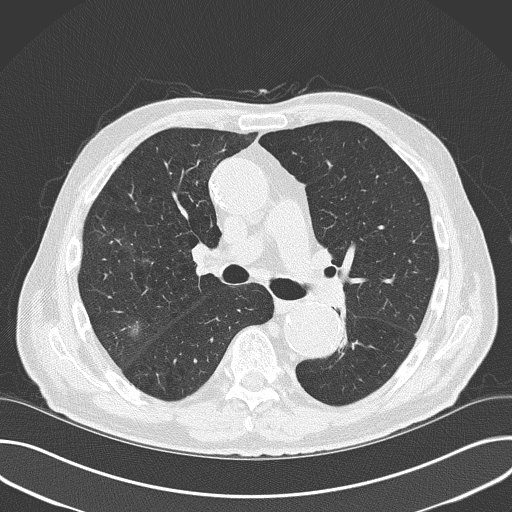
Low-dose screening chest CT, one axial slice; position 98 of 177 along the scan axis; reconstruction kernel B50f; lung window (W 1500 / L -600 HU); 2 mm slice thickness; 512 × 512 image matrix.
Annotated regions visible in this slice (expert manual segmentation):
- lesion 1 (tumor, upper lobe of right lung): bounding box <128,328,139,329> (left, top, right, bottom; pixels)